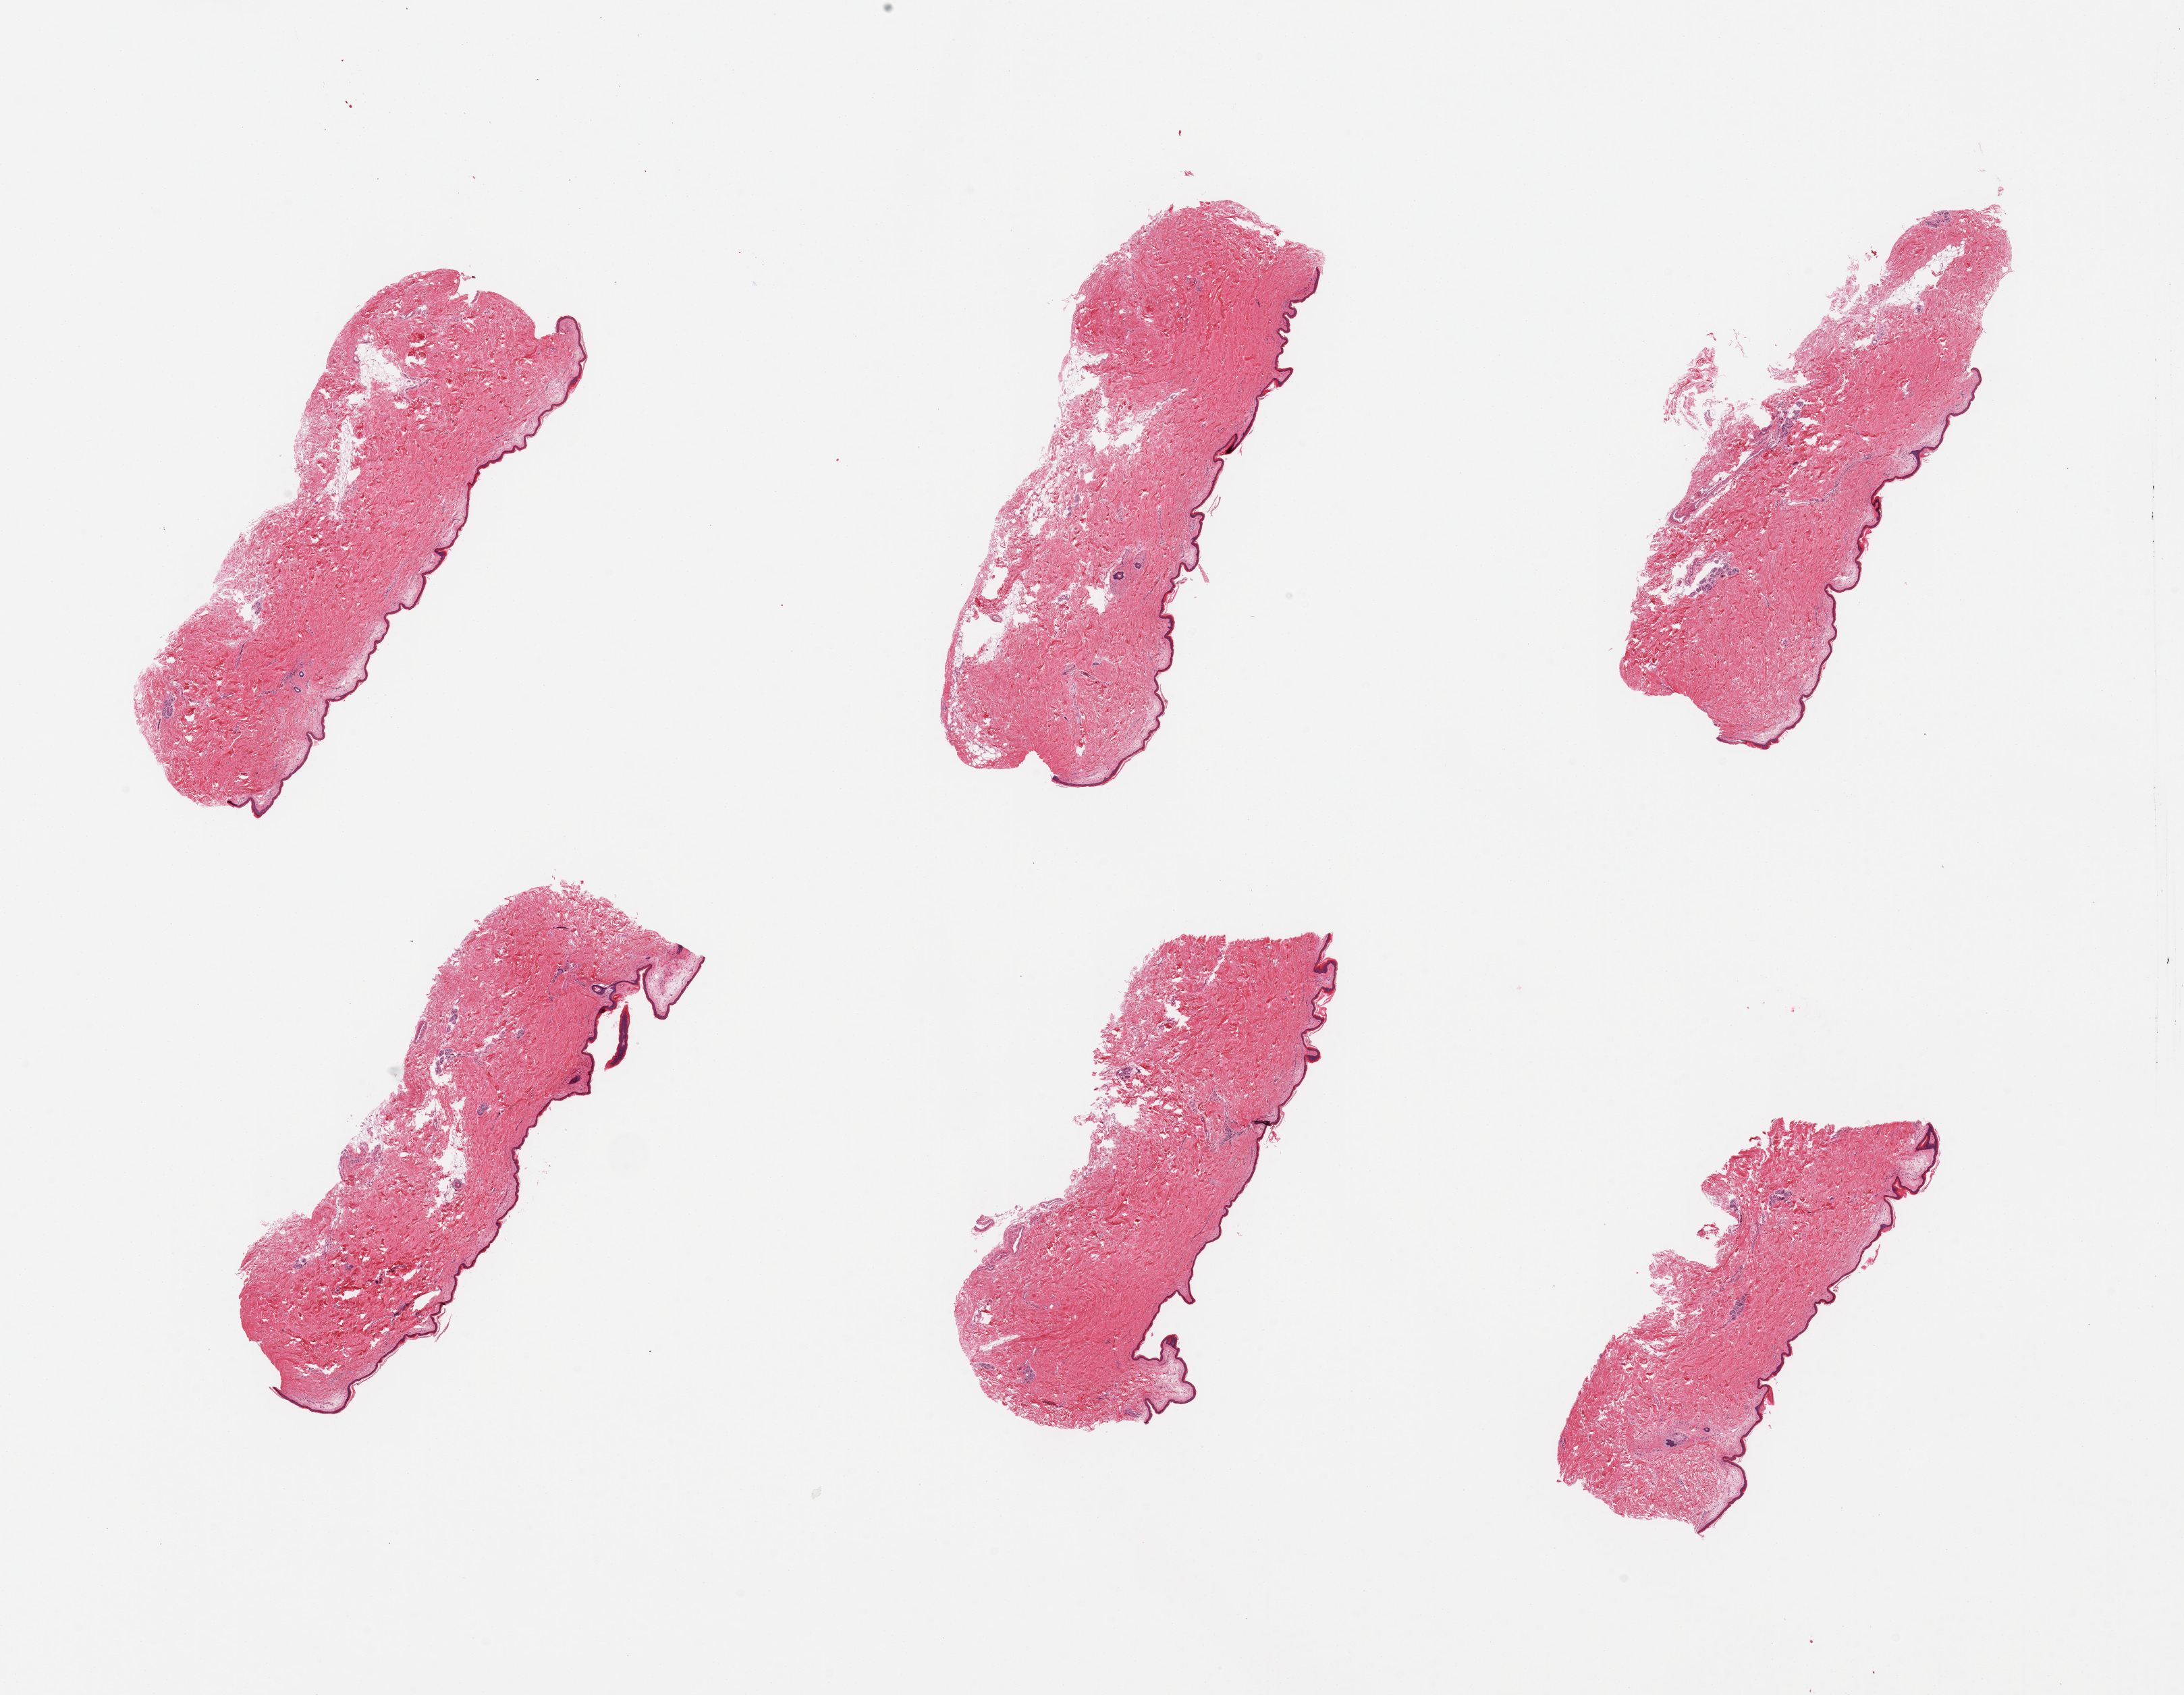
Whole-slide image, haematoxylin and eosin stain — whole scanned area (about 25.6 x 19.9 mm, slide scanned at 20x) shown as a low-resolution overview. PAXgene-fixed, paraffin-embedded tissue. Target tissue: skin of suprapubic region. Donor tissue sample. Female donor.
* review note (as recorded): 2 pieces; well-trimmed, but with small portion of intradermal fat